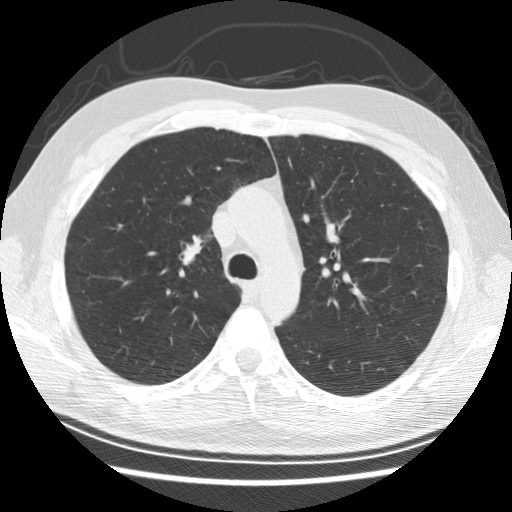
Low-dose screening chest CT, axial slice. Baseline screening round. Lung window (W 1500 / L -600 HU). 2.5 mm slice thickness. 120 kVp. Slice 89 of 278 in the series. 512 × 512 image matrix. Male participant, aged 57 years at enrolment. Former smoker at enrolment.
Lesion marked by an expert reader, bounding box [x1, y1, x2, y2] px = [164, 221, 222, 278]. The screening reader recorded 6 non-calcified nodules or masses ≥4 mm on this exam (right middle lobe, right middle lobe, right lower lobe, right middle lobe, right middle lobe, right lower lobe); which of them this box marks is not recorded. Official screen result: negative screen, minor abnormalities not suspicious for lung cancer. Participant outcome: lung cancer diagnosed 766 days after this screen — adenocarcinoma, NOS, right upper lobe, poorly differentiated (G3), stage IB (AJCC 6th edition), 25 mm at pathology.